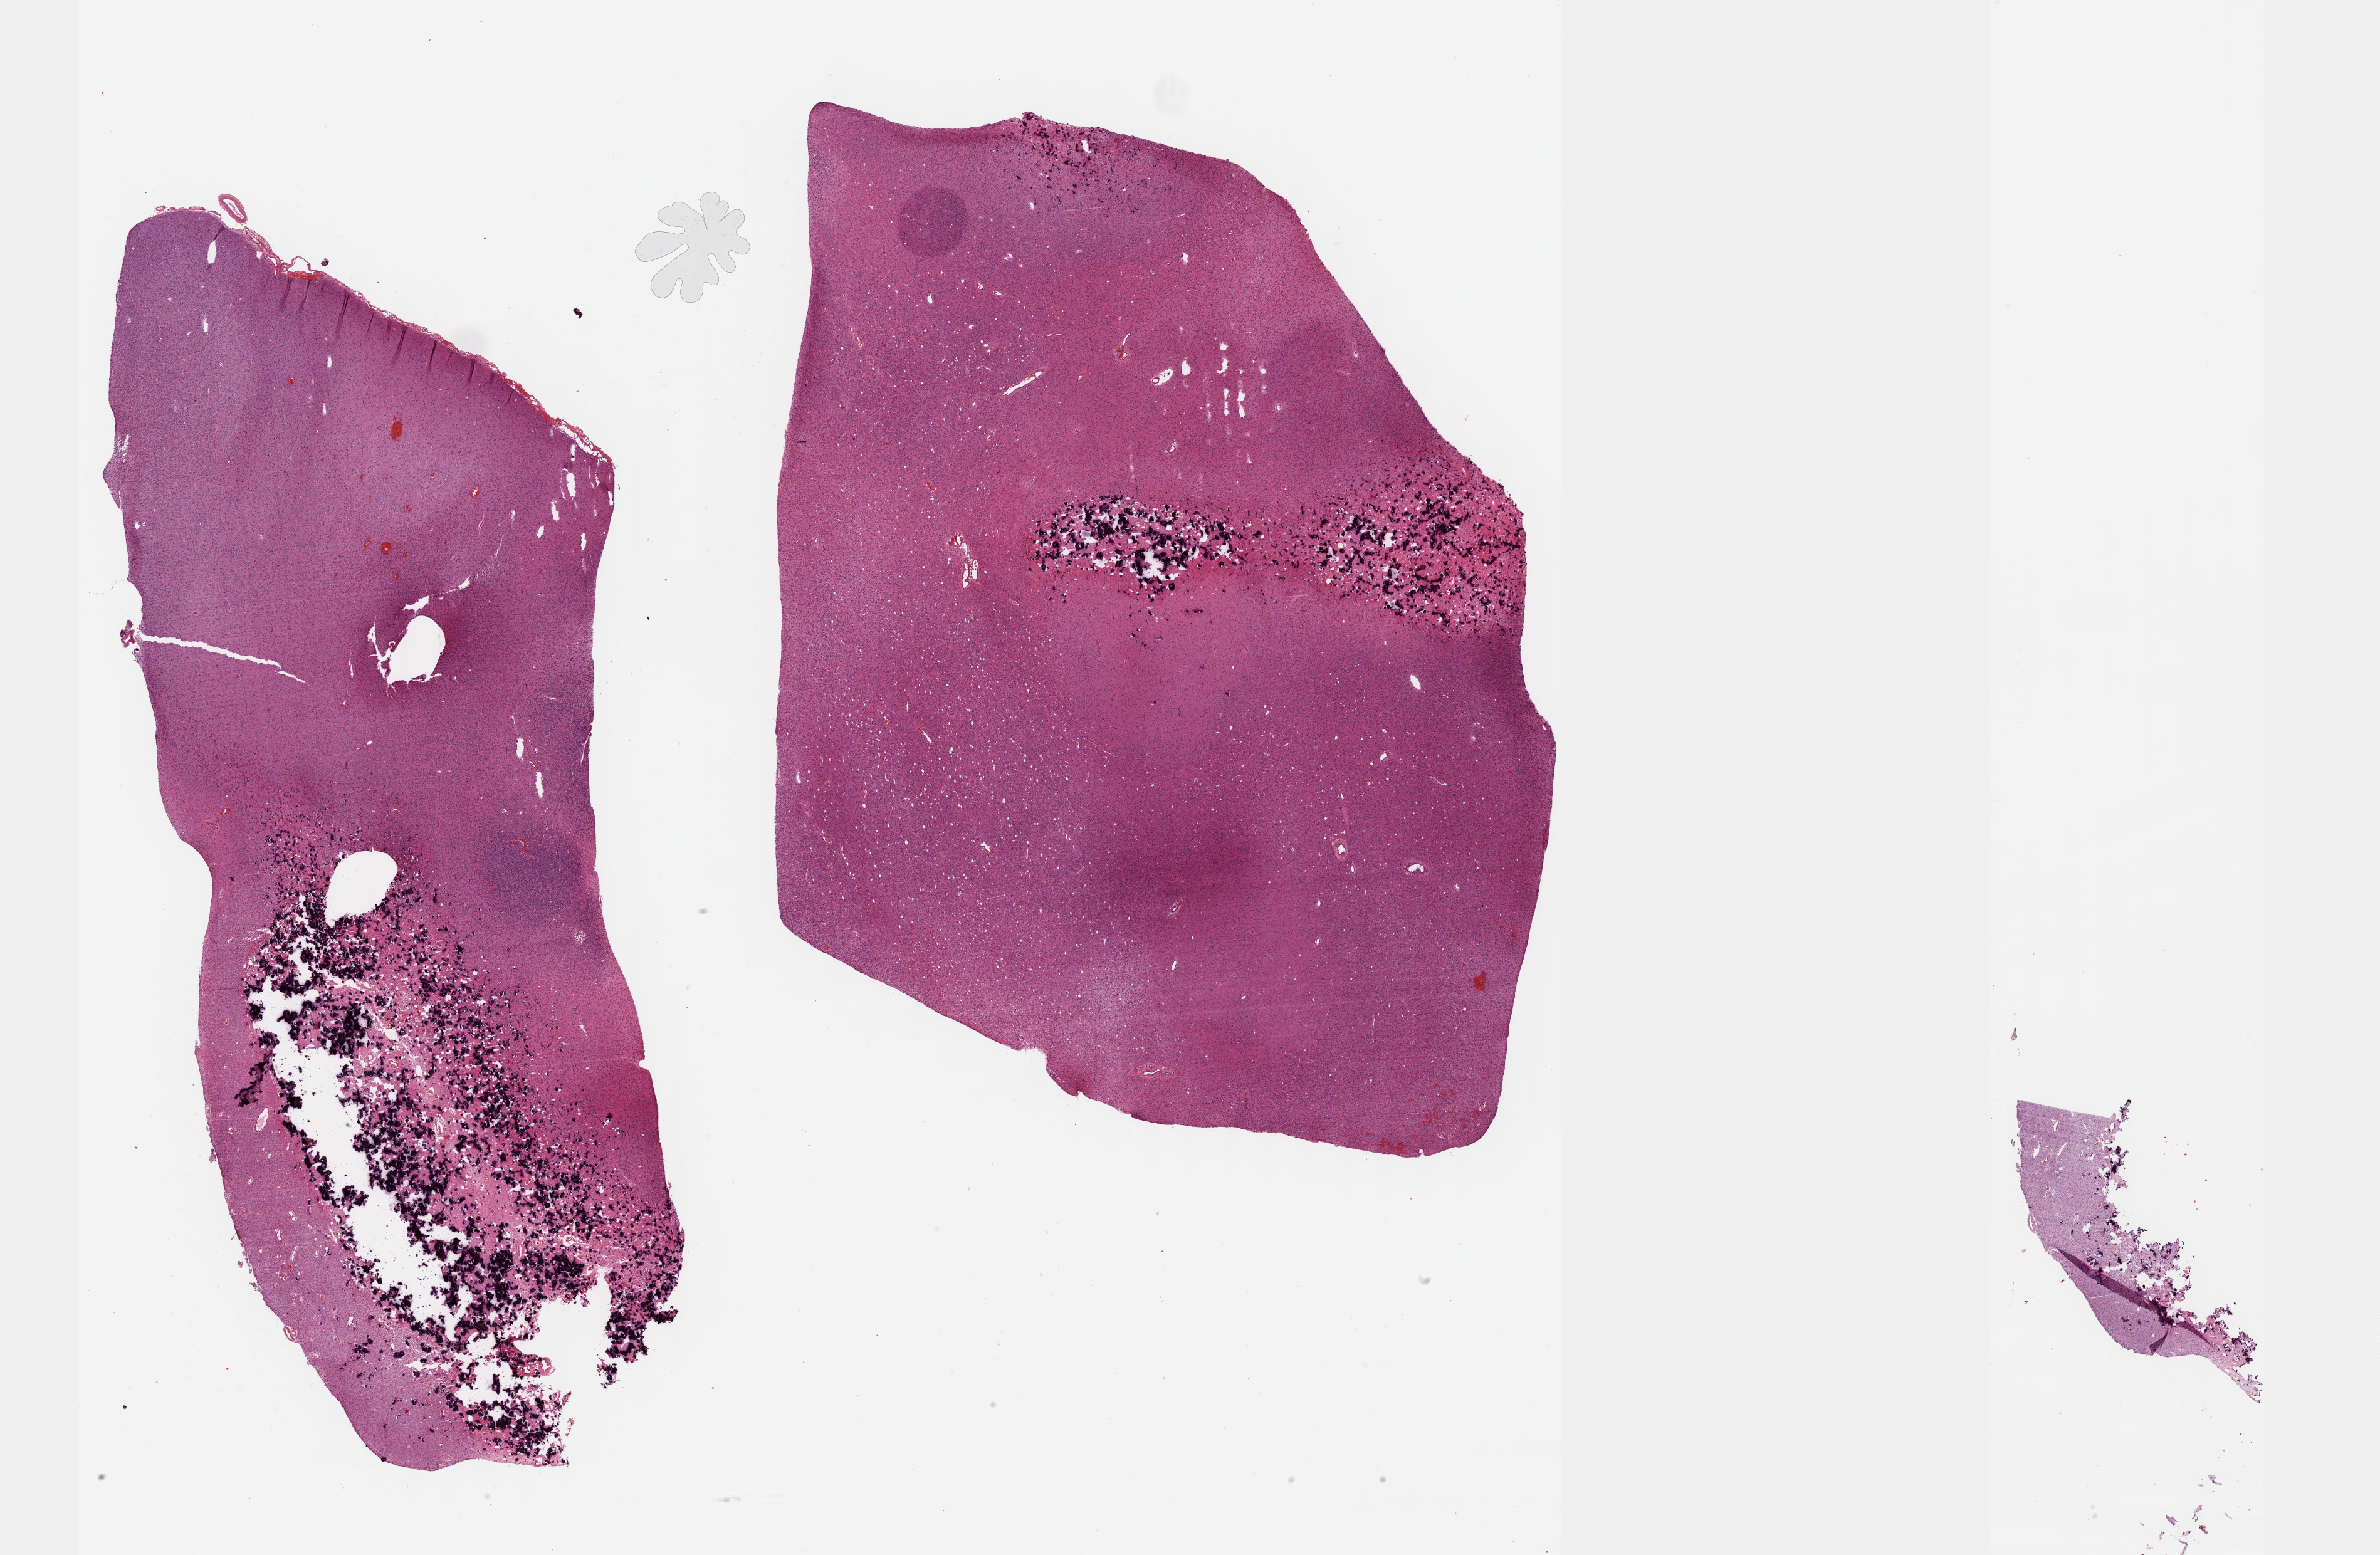
H&E-stained whole-slide image, whole scanned area (about 30.7 x 20.0 mm, slide scanned at 40x) shown as a low-resolution overview, formalin-fixed paraffin-embedded (FFPE) diagnostic section, sample: primary tumour, brain. Female patient; age at initial diagnosis 41 years. Histologic grade: G3 (poorly differentiated).
Diagnosis: Oligodendroglioma, anaplastic.